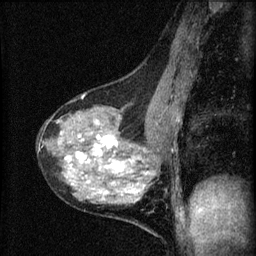
Breast MRI (dynamic contrast-enhanced), one sagittal slice; position 32 of 60 along the scan axis; dynamic contrast-enhanced series, image 2 of 4 at this slice position (ordered by acquisition); 1.5 T; TE 4.2 ms, TR 8.2 ms; 2 mm slice thickness; 256 × 256 image matrix, field of view 180 × 180 mm. Patient: female, 41 years.
Annotated regions visible in this slice (semi-automatic segmentation, software-assisted and operator-edited):
- analysis volume of interest (the breast-tissue region the enhancement analysis was run in; not a lesion): bounding box [x1, y1, x2, y2] px = [38, 91, 166, 209]
- tumour enhancement mask (voxels above the 70 % enhancement threshold inside the analysis volume of interest): [64, 133, 147, 194]